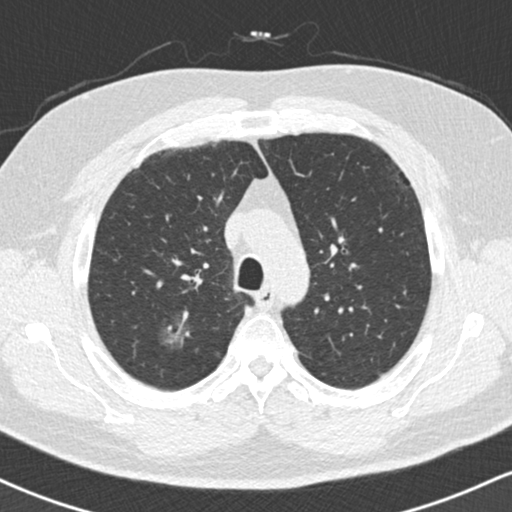
Low-dose screening chest CT, axial slice, second annual screen, lung window (W 1500 / L -600 HU), 2 mm slice thickness, 512 × 512 image matrix, field of view 320 × 320 mm. Male participant, aged 59 years at enrolment. Current smoker at enrolment.
Expert-annotated lung lesion, bounding box <153,304,208,361> (left, top, right, bottom; pixels). Screening reader's record for this exam (one nodule recorded; not confirmed to be the boxed lesion): non-calcified nodule or mass ≥4 mm, right upper lobe, 18 × 16 mm, ground glass attenuation, pre-existing on the prior screen: yes. Official screen result: positive, no significant change: stable abnormalities potentially related to lung cancer, unchanged since the prior screening exam. Participant outcome: lung cancer diagnosed 60 days after this screen — bronchiolo-alveolar adenocarcinoma, NOS, right lower lobe, stage IA (AJCC 6th edition), 15 mm at pathology.